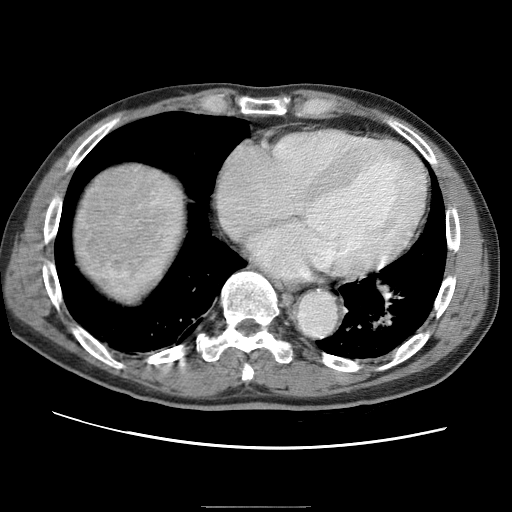
Contrast-enhanced abdominal CT (liver protocol), one axial slice. Slice 67 of 75 in the series (ordered by position). 120 kVp. One of 2 acquisitions stored at this slice position. Soft-tissue window (W 400 / L 40 HU). 2.5 mm slice thickness. 512 × 512 image matrix, field of view 360 × 360 mm. Case-level facts recorded for this patient, not image findings: diagnosis: hepatocellular carcinoma (patient treated with transarterial chemoembolisation; whether this scan precedes or follows treatment is not stated here); TNM stage (as recorded): Stage-II; Child-Pugh class: A; tumour differentiation: well differentiated; tumour nodularity: multinodular.
Annotated regions visible in this slice (semi-automatic segmentation, software-assisted and operator-edited):
- liver parenchyma outside the tumour (the mass and vessels are separate outlines, so this box may not span the whole liver): box from (x=68, y=156) to (x=196, y=304) px
- mass: (x=69, y=160)–(x=170, y=289)
- liver vessels: (x=176, y=211)–(x=179, y=215)